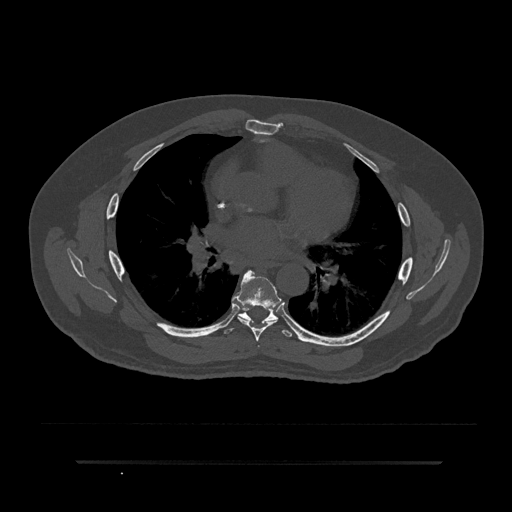
CT including the spine, one axial slice. Slice 508 of 797 in the series (ordered by position). Reconstruction kernel Br40s/3. 120 kVp. Bone window (W 1800 / L 400 HU). 0.5 mm slice thickness. 512 × 512 image matrix. Patient: male, 59 years. From the clinical record (not read from this slice): primary cancer: bile ducts.
Outlined on this slice (semi-automatically segmented with operator editing):
- T6 vertebra: bounding box (x1, y1, x2, y2) in pixels: (232, 270, 282, 342)
- T7 vertebra: (224, 306, 295, 337)